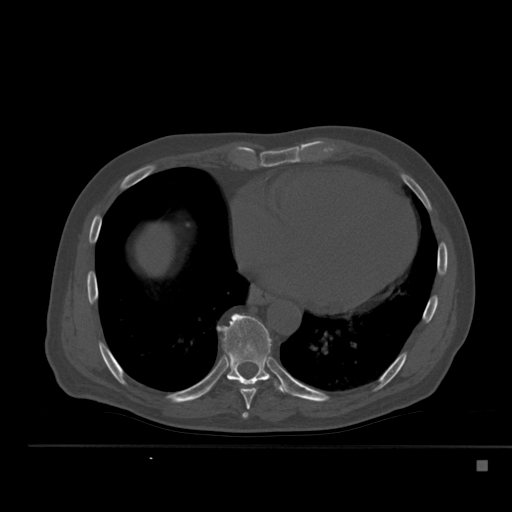
CT including the spine, one axial slice; position 297 of 517 along the scan axis; 120 kVp; bone window (W 1800 / L 400 HU); 1.5 mm slice thickness; 512 × 512 image matrix, field of view 408 × 408 mm. Patient: male, 70 years. From the clinical record (not read from this slice): primary cancer: renal.
Outlined on this slice (semi-automatic segmentation, software-assisted and operator-edited):
- T7 vertebra: box from (x=242, y=412) to (x=249, y=418) px
- T8 vertebra: (x=234, y=380)–(x=261, y=410)
- T9 vertebra: (x=217, y=314)–(x=284, y=393)